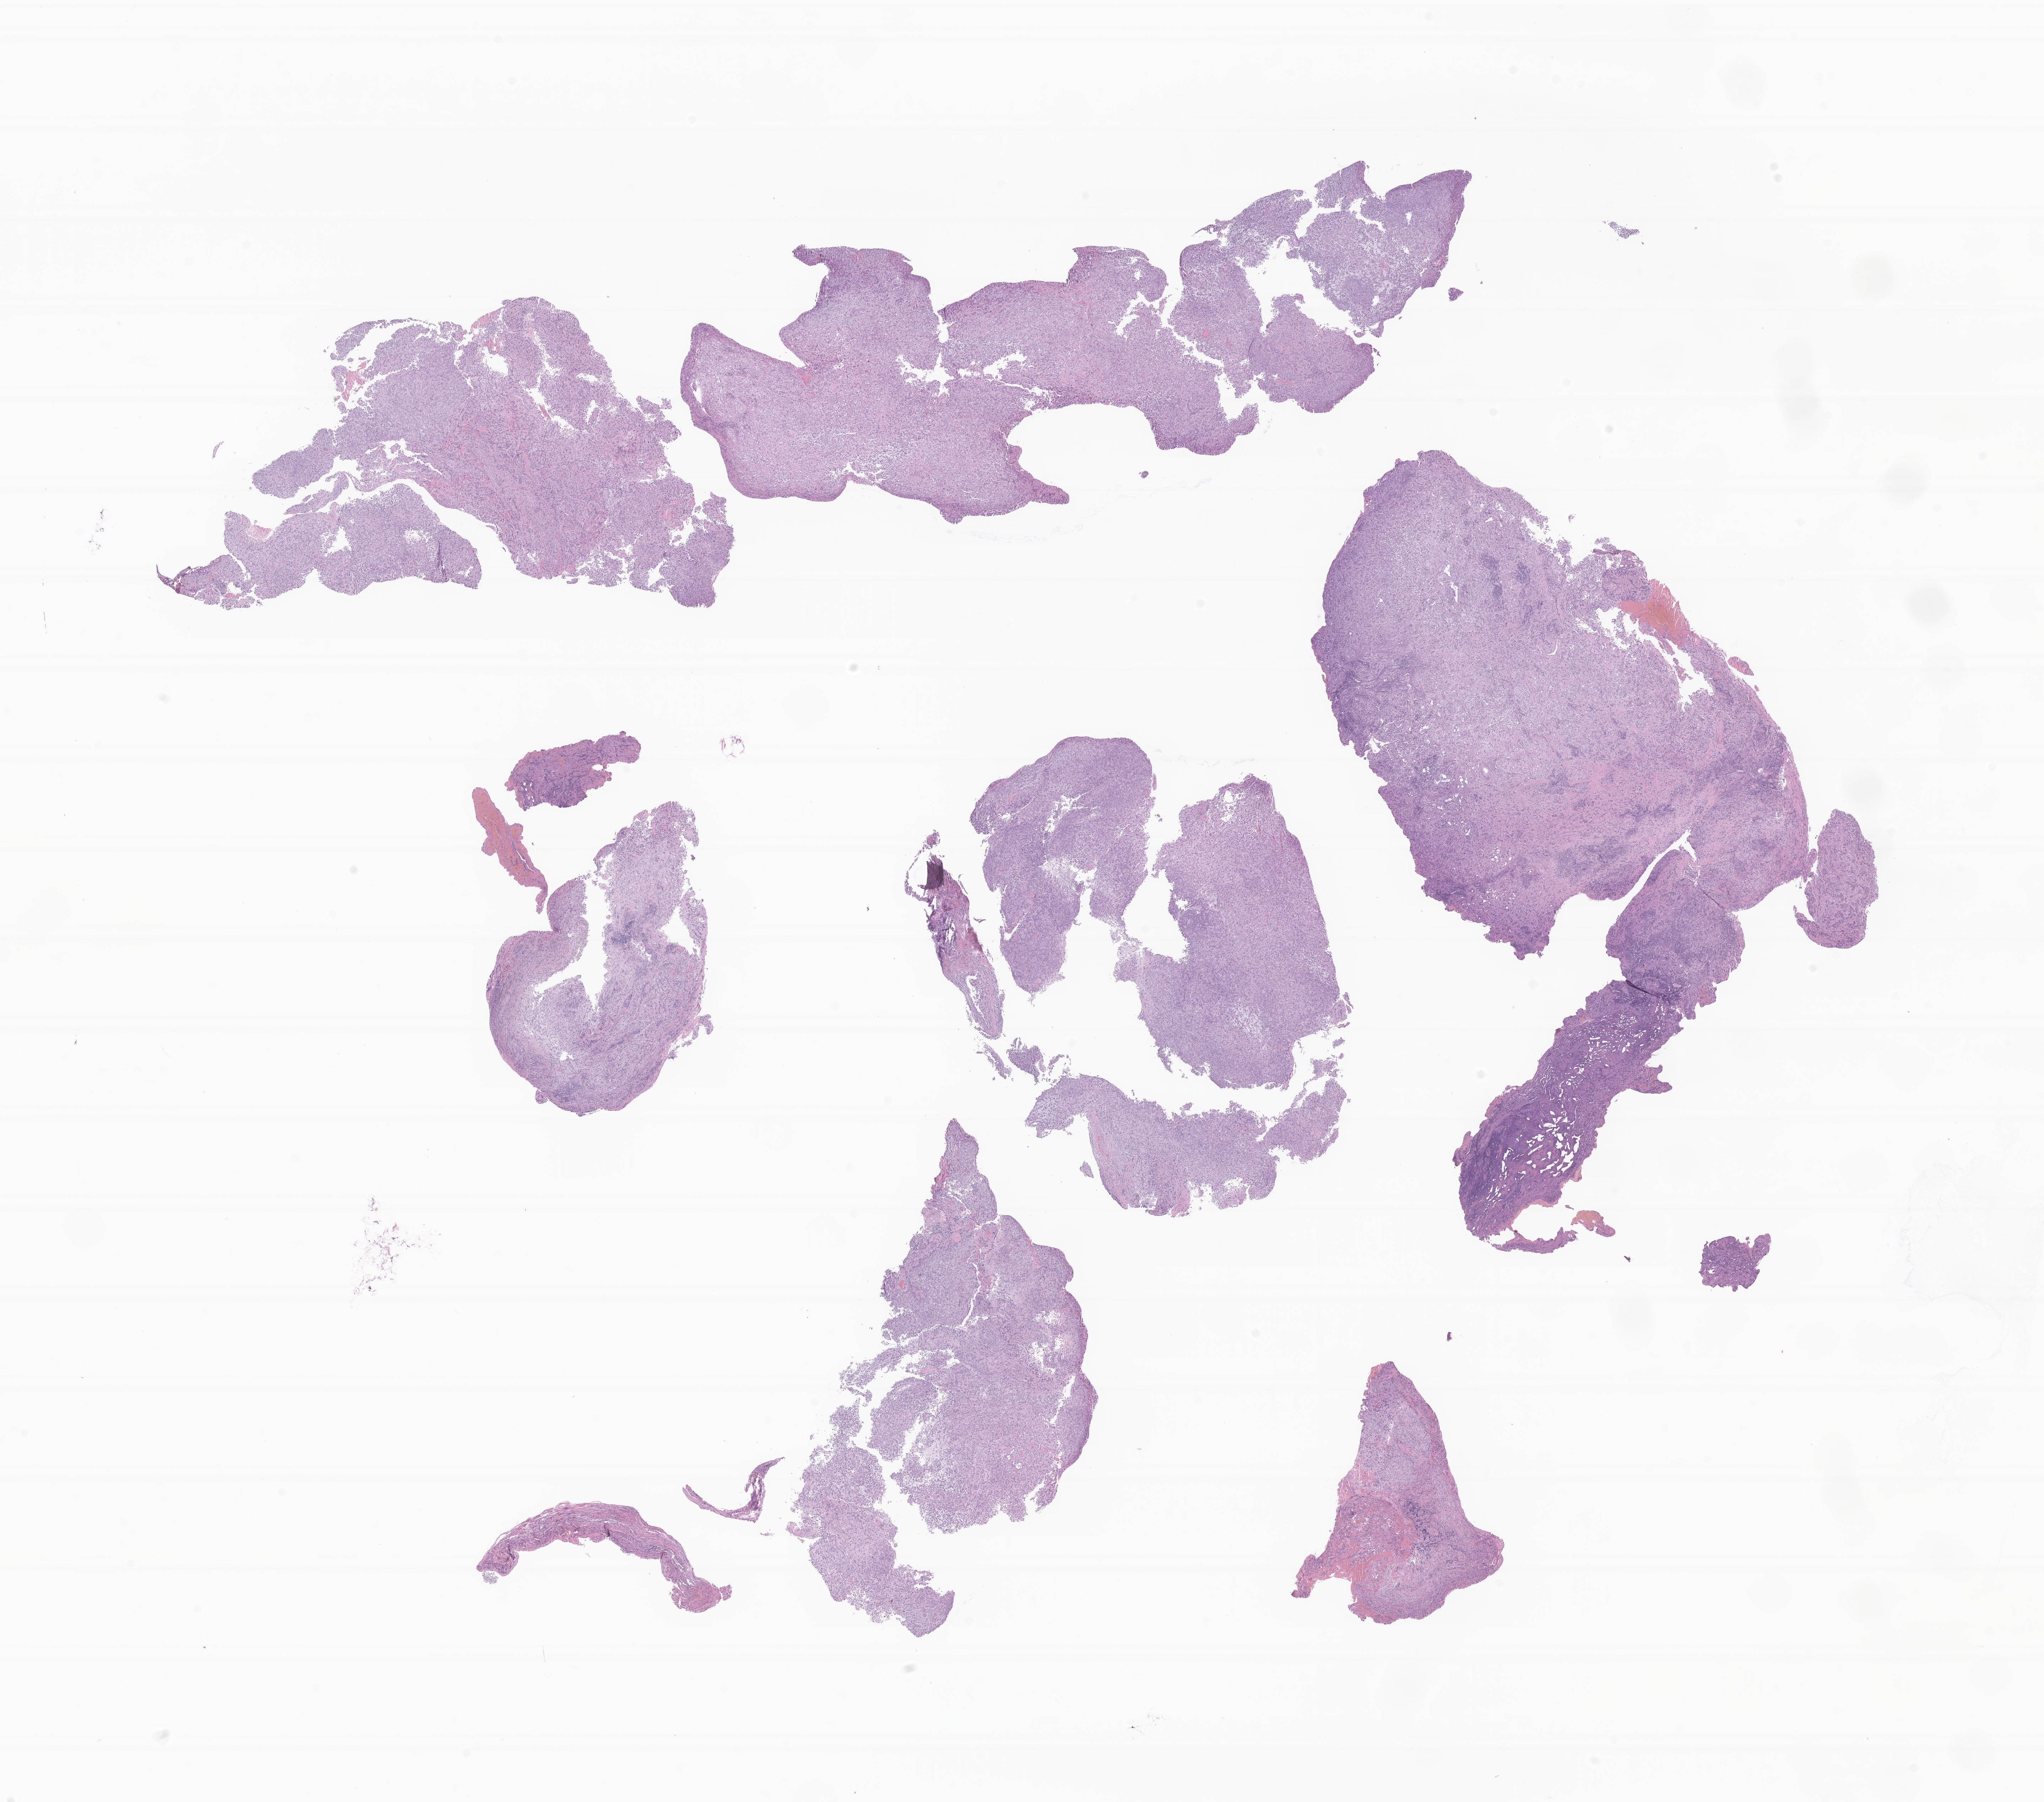
Hematoxylin and eosin (H&E) whole-slide image of tumor tissue from the spinal cord, a low-resolution overview of the entire scanned area, about 24.3 x 21.4 mm. FFPE section. Patient female; age 213 months (17 years 9 months).
Diagnosis: Mesenchymoma, NOS.